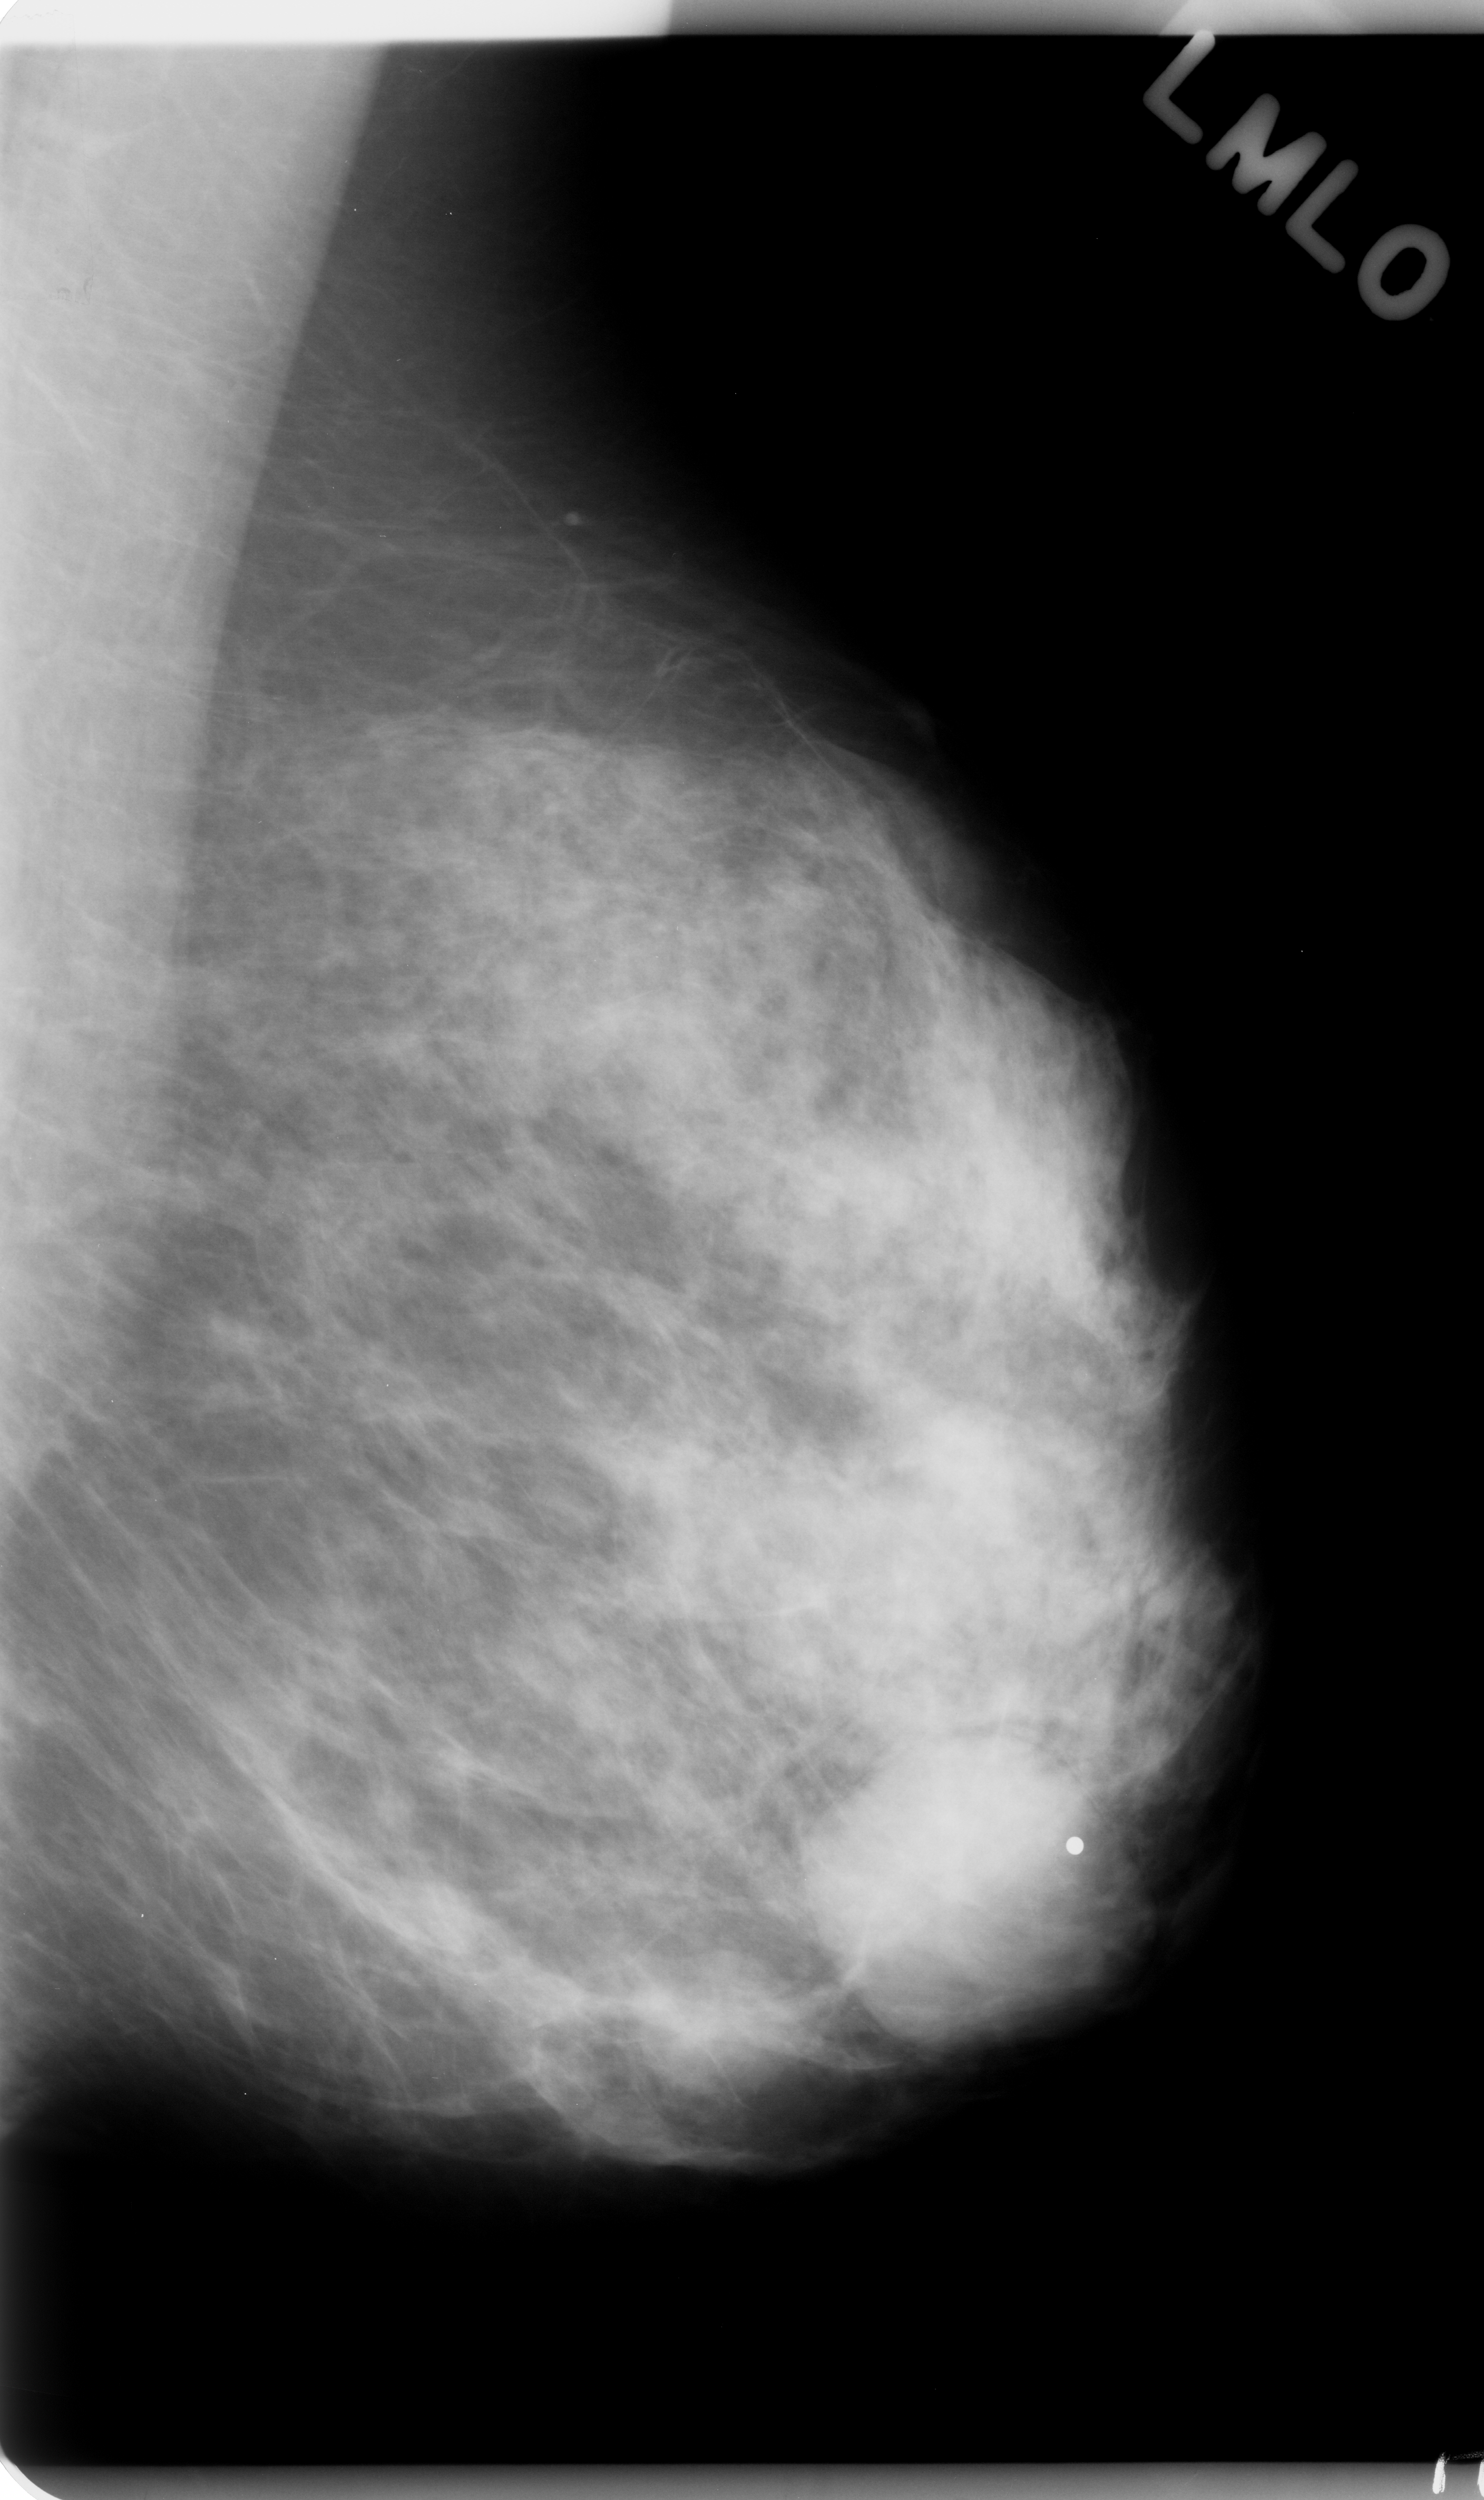
Scanned film-screen mammogram, left breast, MLO view, BI-RADS breast density category 2 (scale 1–4).
- Mass, shape round, margins circumscribed; BI-RADS assessment category 4; subtlety rating 3 on a 1 (subtle) to 5 (obvious) scale; pathology result (as recorded, not read from the image): benign.